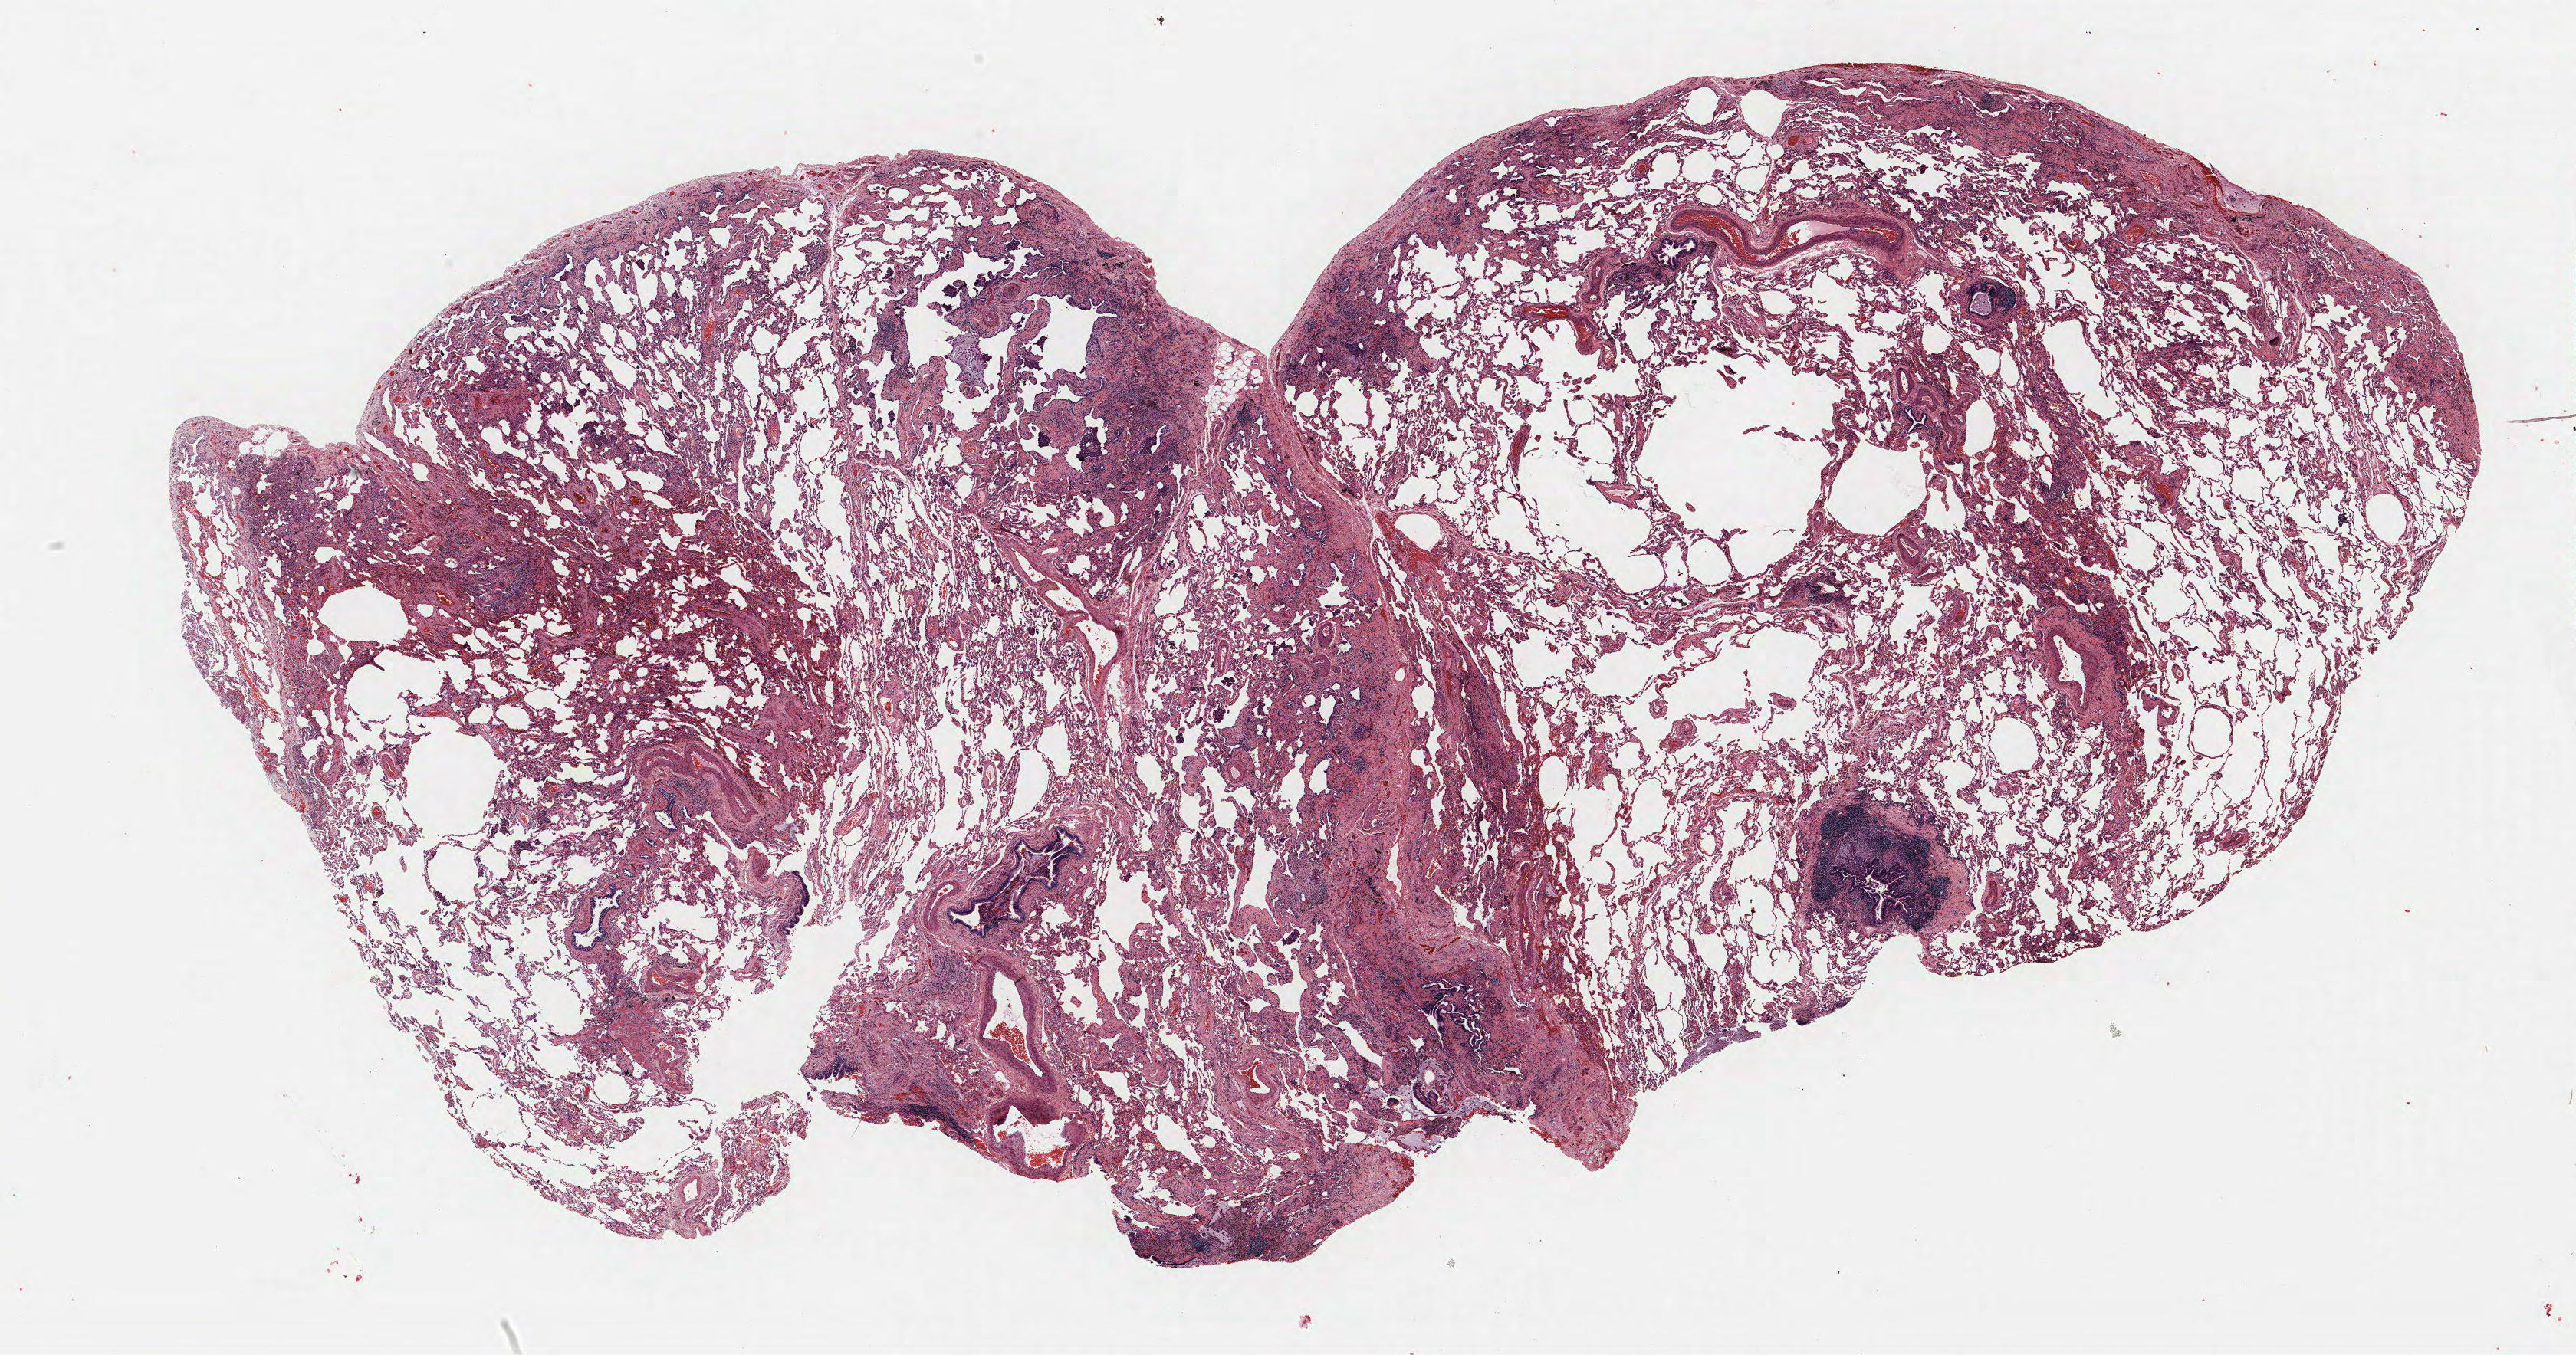
H&E-stained whole-slide image, low-resolution overview of the scanned area, about 26.9 x 14.1 mm (acquisition: 40x scan). FFPE section. Lung tissue. Male patient, aged 68 at enrolment. Current smoker at enrolment. Grade: moderately differentiated (G2).
Primary tumour location (clinical record): right upper lobe. Tumour size (pathology): 7 mm. Stage (AJCC 6th edition): IIIA. Participant's lung-cancer diagnosis: Squamous cell carcinoma, NOS (ICD-O-3 8070/3).